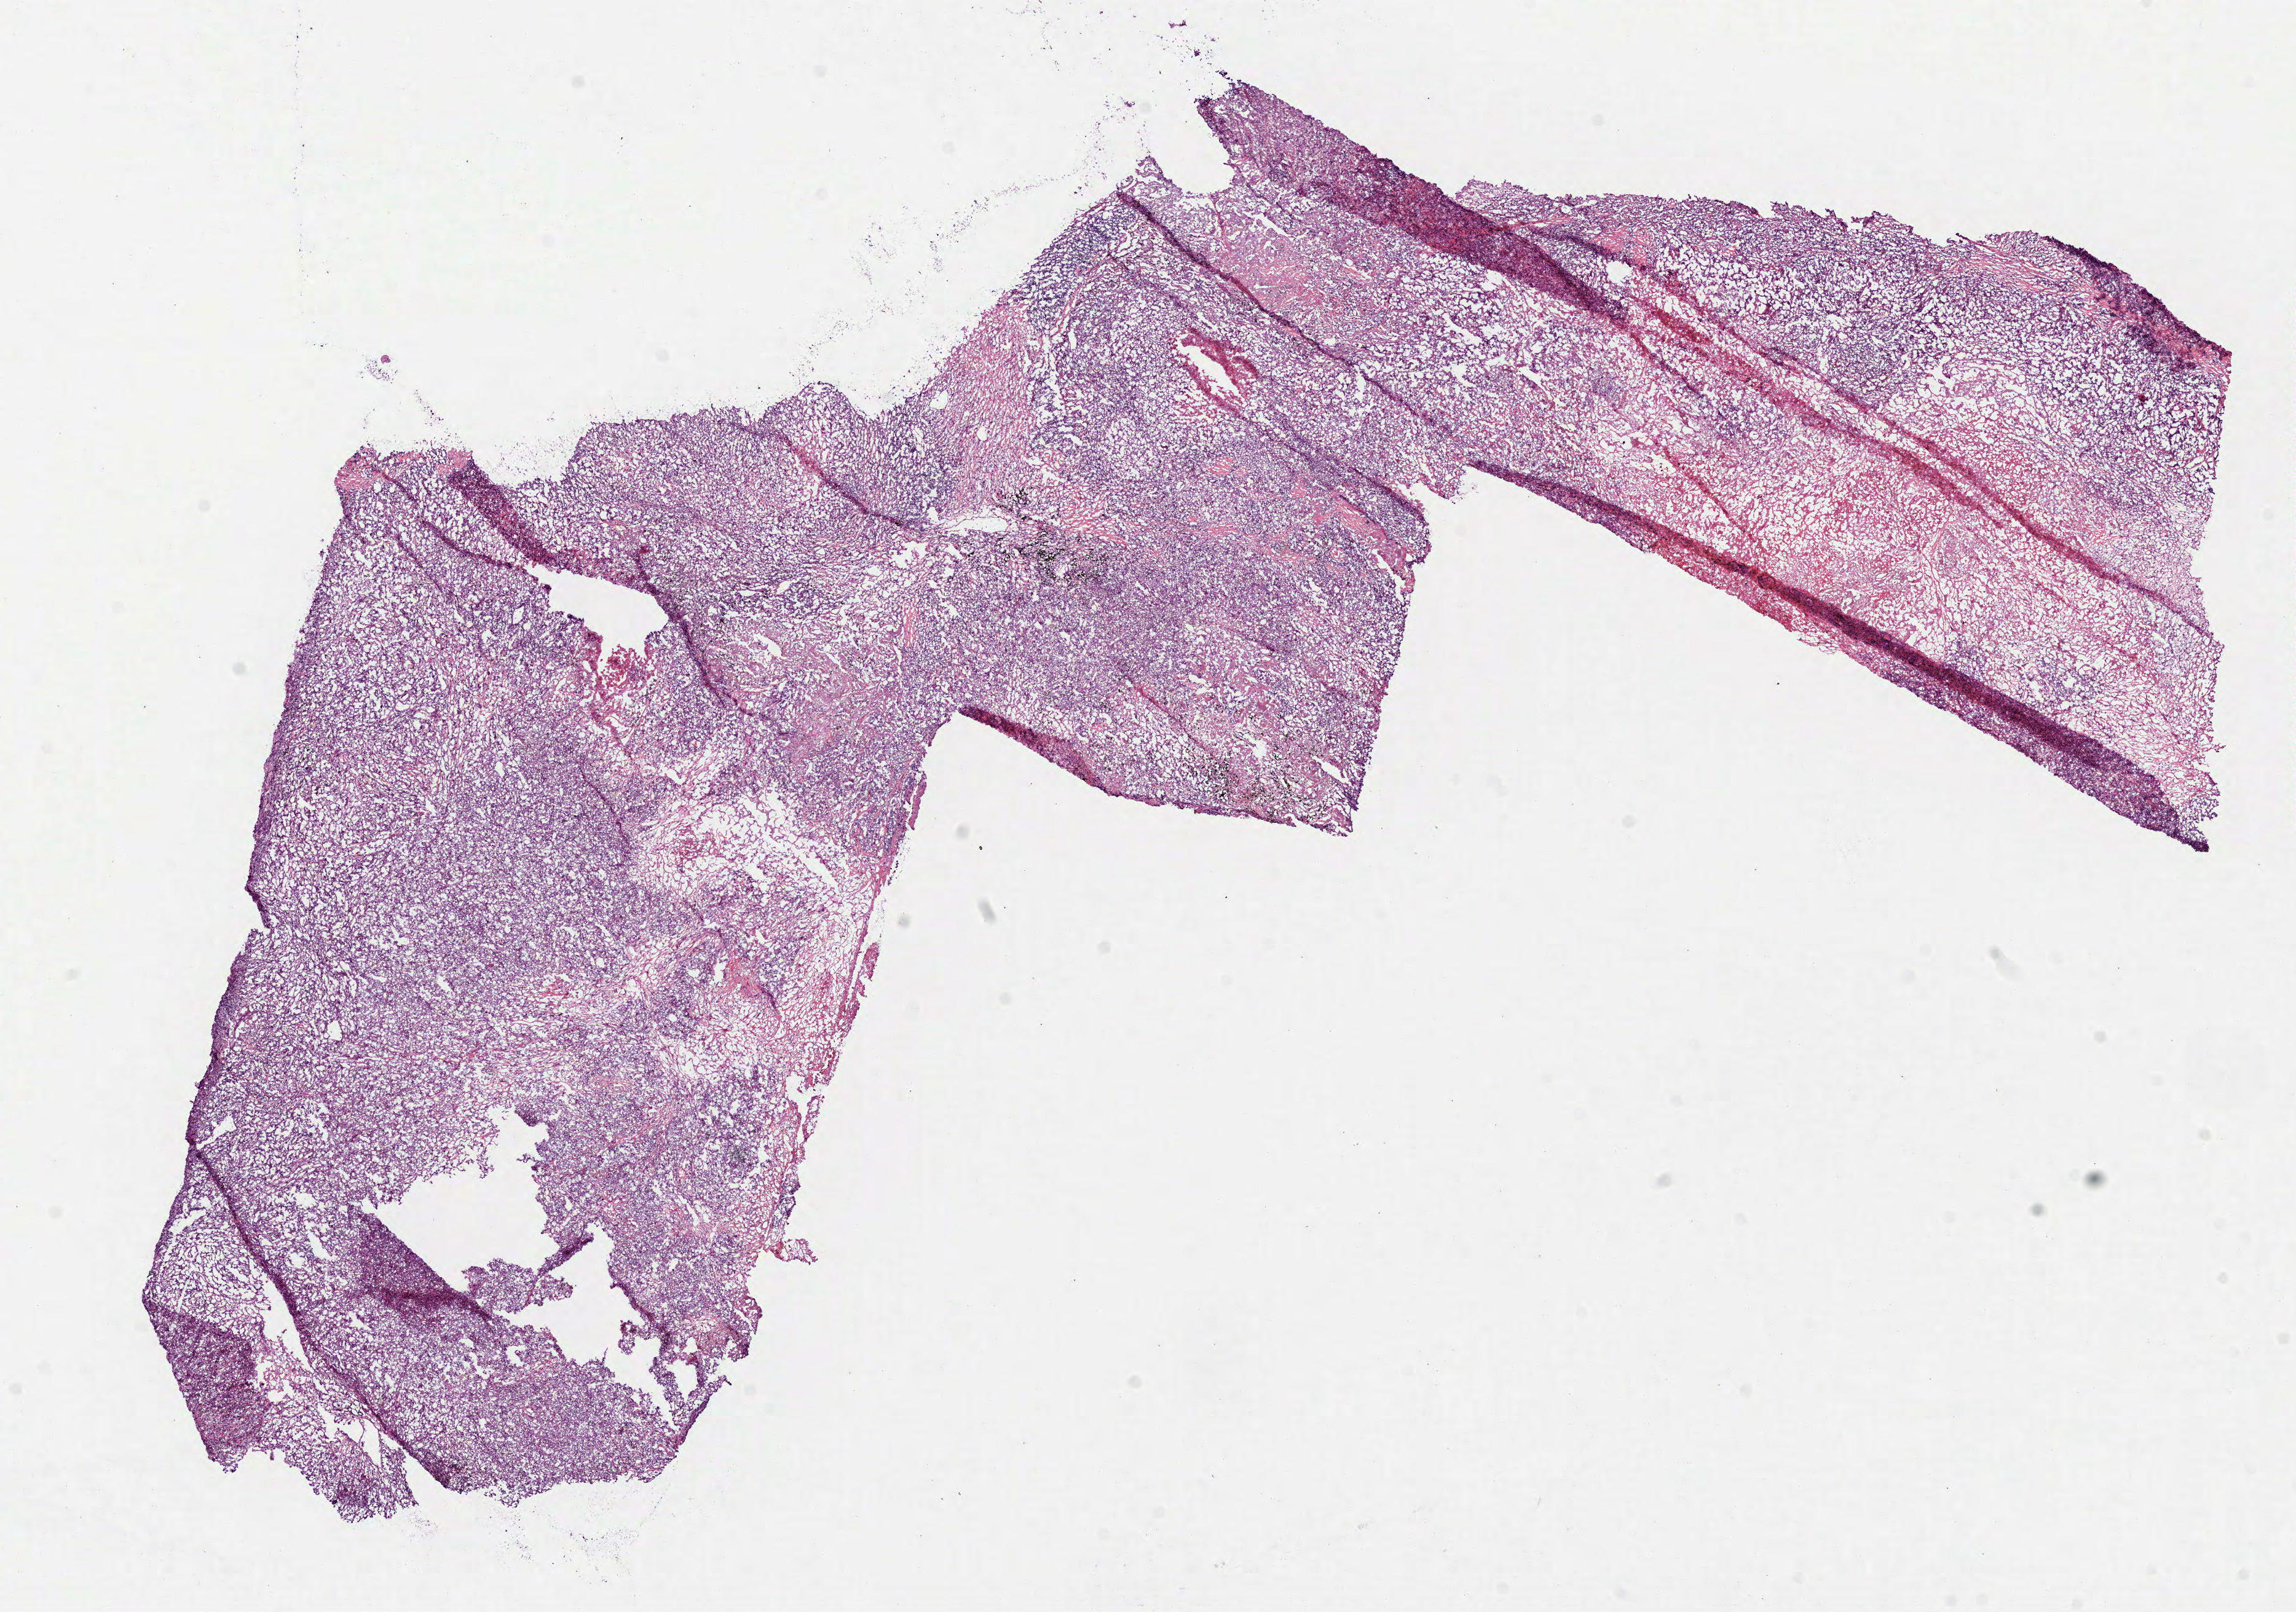
Digitized Hematoxylin and eosin (H&E) stained tissue section (whole slide) — shown as a low-resolution overview of the whole scanned area (about 15.1 x 10.6 mm). Frozen section from the top of the tissue portion. Primary tumour sample from the lung. Female, age 72 years at initial diagnosis. Pathologist review of this section (percent, as recorded): tumour cells 80%, tumour nuclei 80%, normal cells 0%, stromal cells 20%, necrosis 0%.
- TNM: T2 N0 M0
- histologic diagnosis: Adenocarcinoma, NOS (upper lobe, lung)
- AJCC pathologic stage: IB (6th edition)